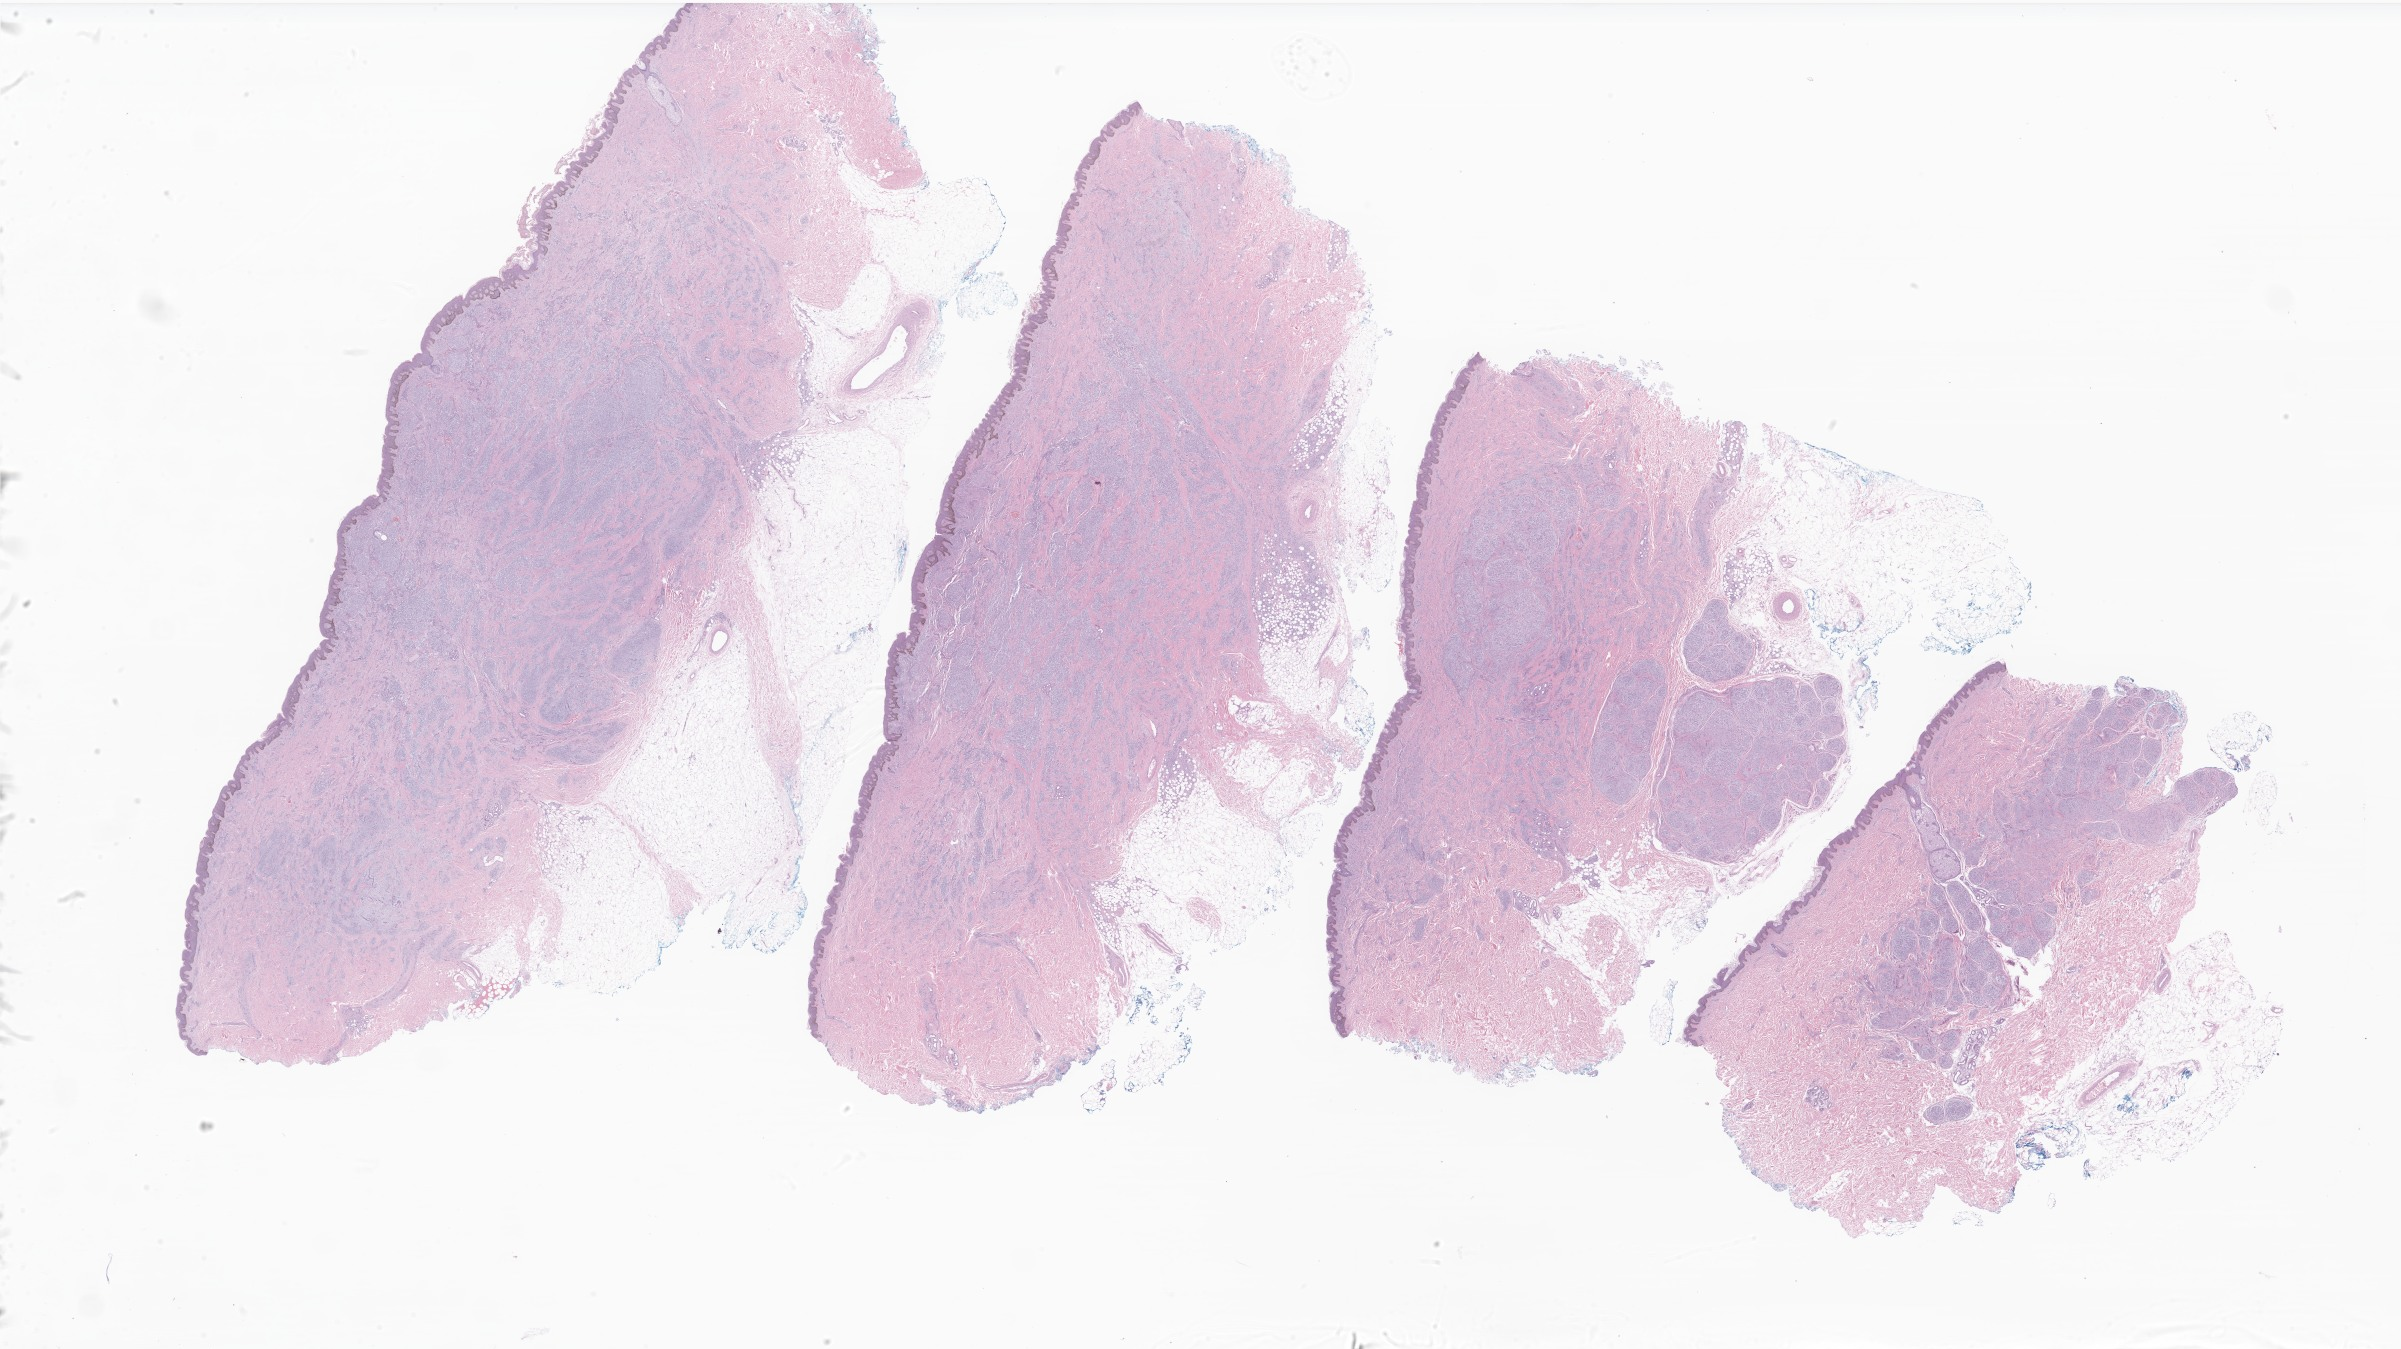
Digitized hematoxylin and eosin (H&E)-stained section of tumor tissue from the soft tissue of lower extremity, shown as a low-resolution overview of the whole scanned area (about 40.5 x 22.8 mm); FFPE section. Female patient, age 195 months (16 years 3 months).
Diagnosis (ICD-O-3 morphology term): Plexiform fibrohistiocytic tumor.